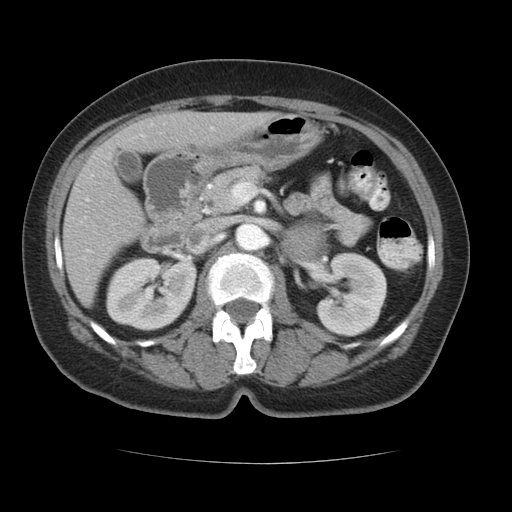
Contrast-enhanced abdominal CT, one axial slice. Position 61 of 96 along the scan axis. Reconstruction kernel STANDARD. Intravenous contrast given. Soft-tissue window (W 400 / L 40 HU). 5 mm slice thickness. 512 × 512 image matrix. Female patient, age 66 years. From the clinical record (not read from this slice): diagnosis: adrenocortical carcinoma; tumour side: left adrenal; tumour size at pathology: 5.5 cm; Ki-67 index: 15 %; stage (as recorded): 3.
Outlined on this slice (semi-automatically segmented with operator editing):
- mass: bounding box (x1, y1, x2, y2) in pixels: (283, 222, 328, 260)